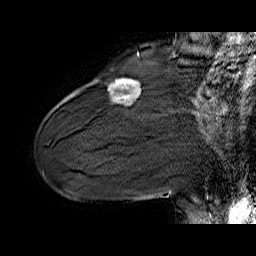
Breast MRI (dynamic contrast-enhanced), one sagittal slice; position 17 of 60 along the scan axis; dynamic contrast-enhanced series, time point 2 of 6 at this slice position (early post-contrast); 1.5 T; TE 6.4 ms, TR 32.9 ms; 4 mm slice thickness; 256 × 256 image matrix, field of view 200 × 200 mm. Female patient. From the clinical record (not read from this slice): setting: breast cancer imaged before/during neoadjuvant chemotherapy; receptor status: HER2-positive.
Structures marked on this image (semi-automatic segmentation, software-assisted and operator-edited):
- analysis volume of interest (the breast-tissue region the enhancement analysis was run in; not a lesion): box from (x=109, y=79) to (x=141, y=105) px
- tumour enhancement mask (voxels above the 100 % enhancement threshold inside the analysis volume of interest): (x=123, y=79)–(x=133, y=82)